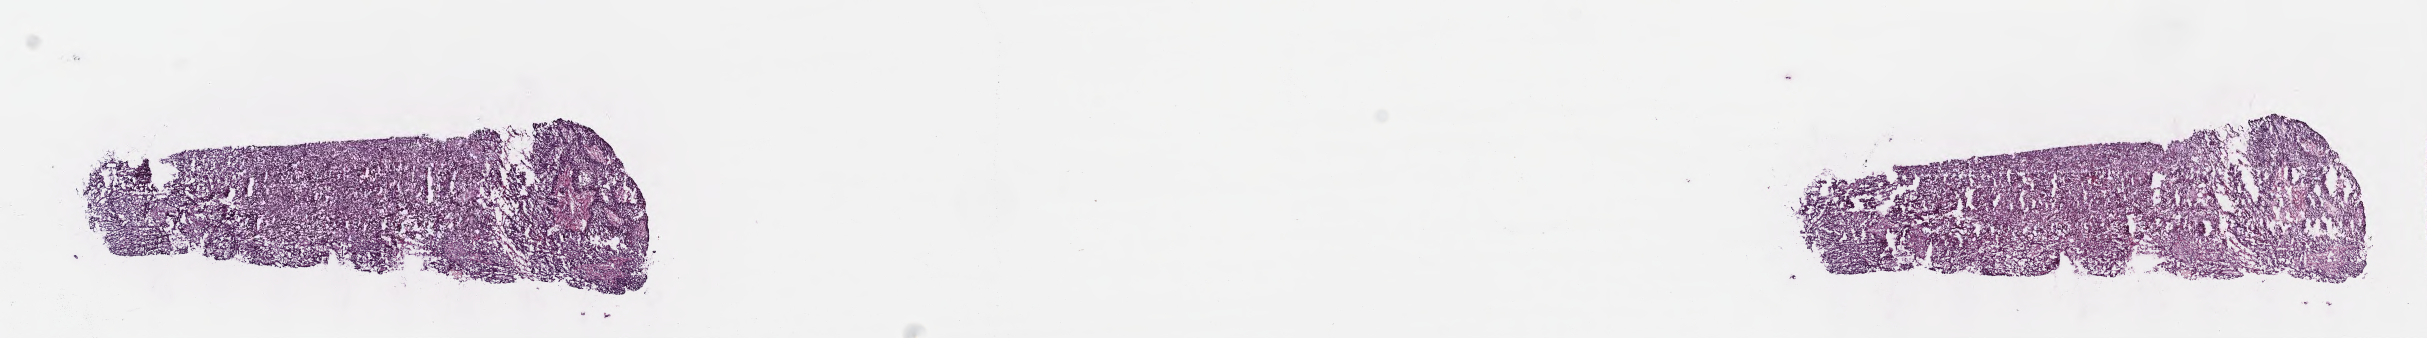
Whole-slide image, haematoxylin and eosin stain, a low-resolution overview of the entire scanned area, about 19.6 x 2.7 mm. Frozen section. Specimen: primary tumor. Site: upper lobe of right lung. Patient male; age 71 years. Slide review estimates, as recorded: tumor cells 60%, tumor nuclei 70%, stromal cells 30%, necrosis 10%, normal cells 0%. Inflammatory infiltration, as recorded: lymphocyte infiltration 5%, monocyte infiltration 3%, neutrophil infiltration 0%.
- AJCC pathologic stage: Stage IB
- diagnosis: Adenocarcinoma, NOS